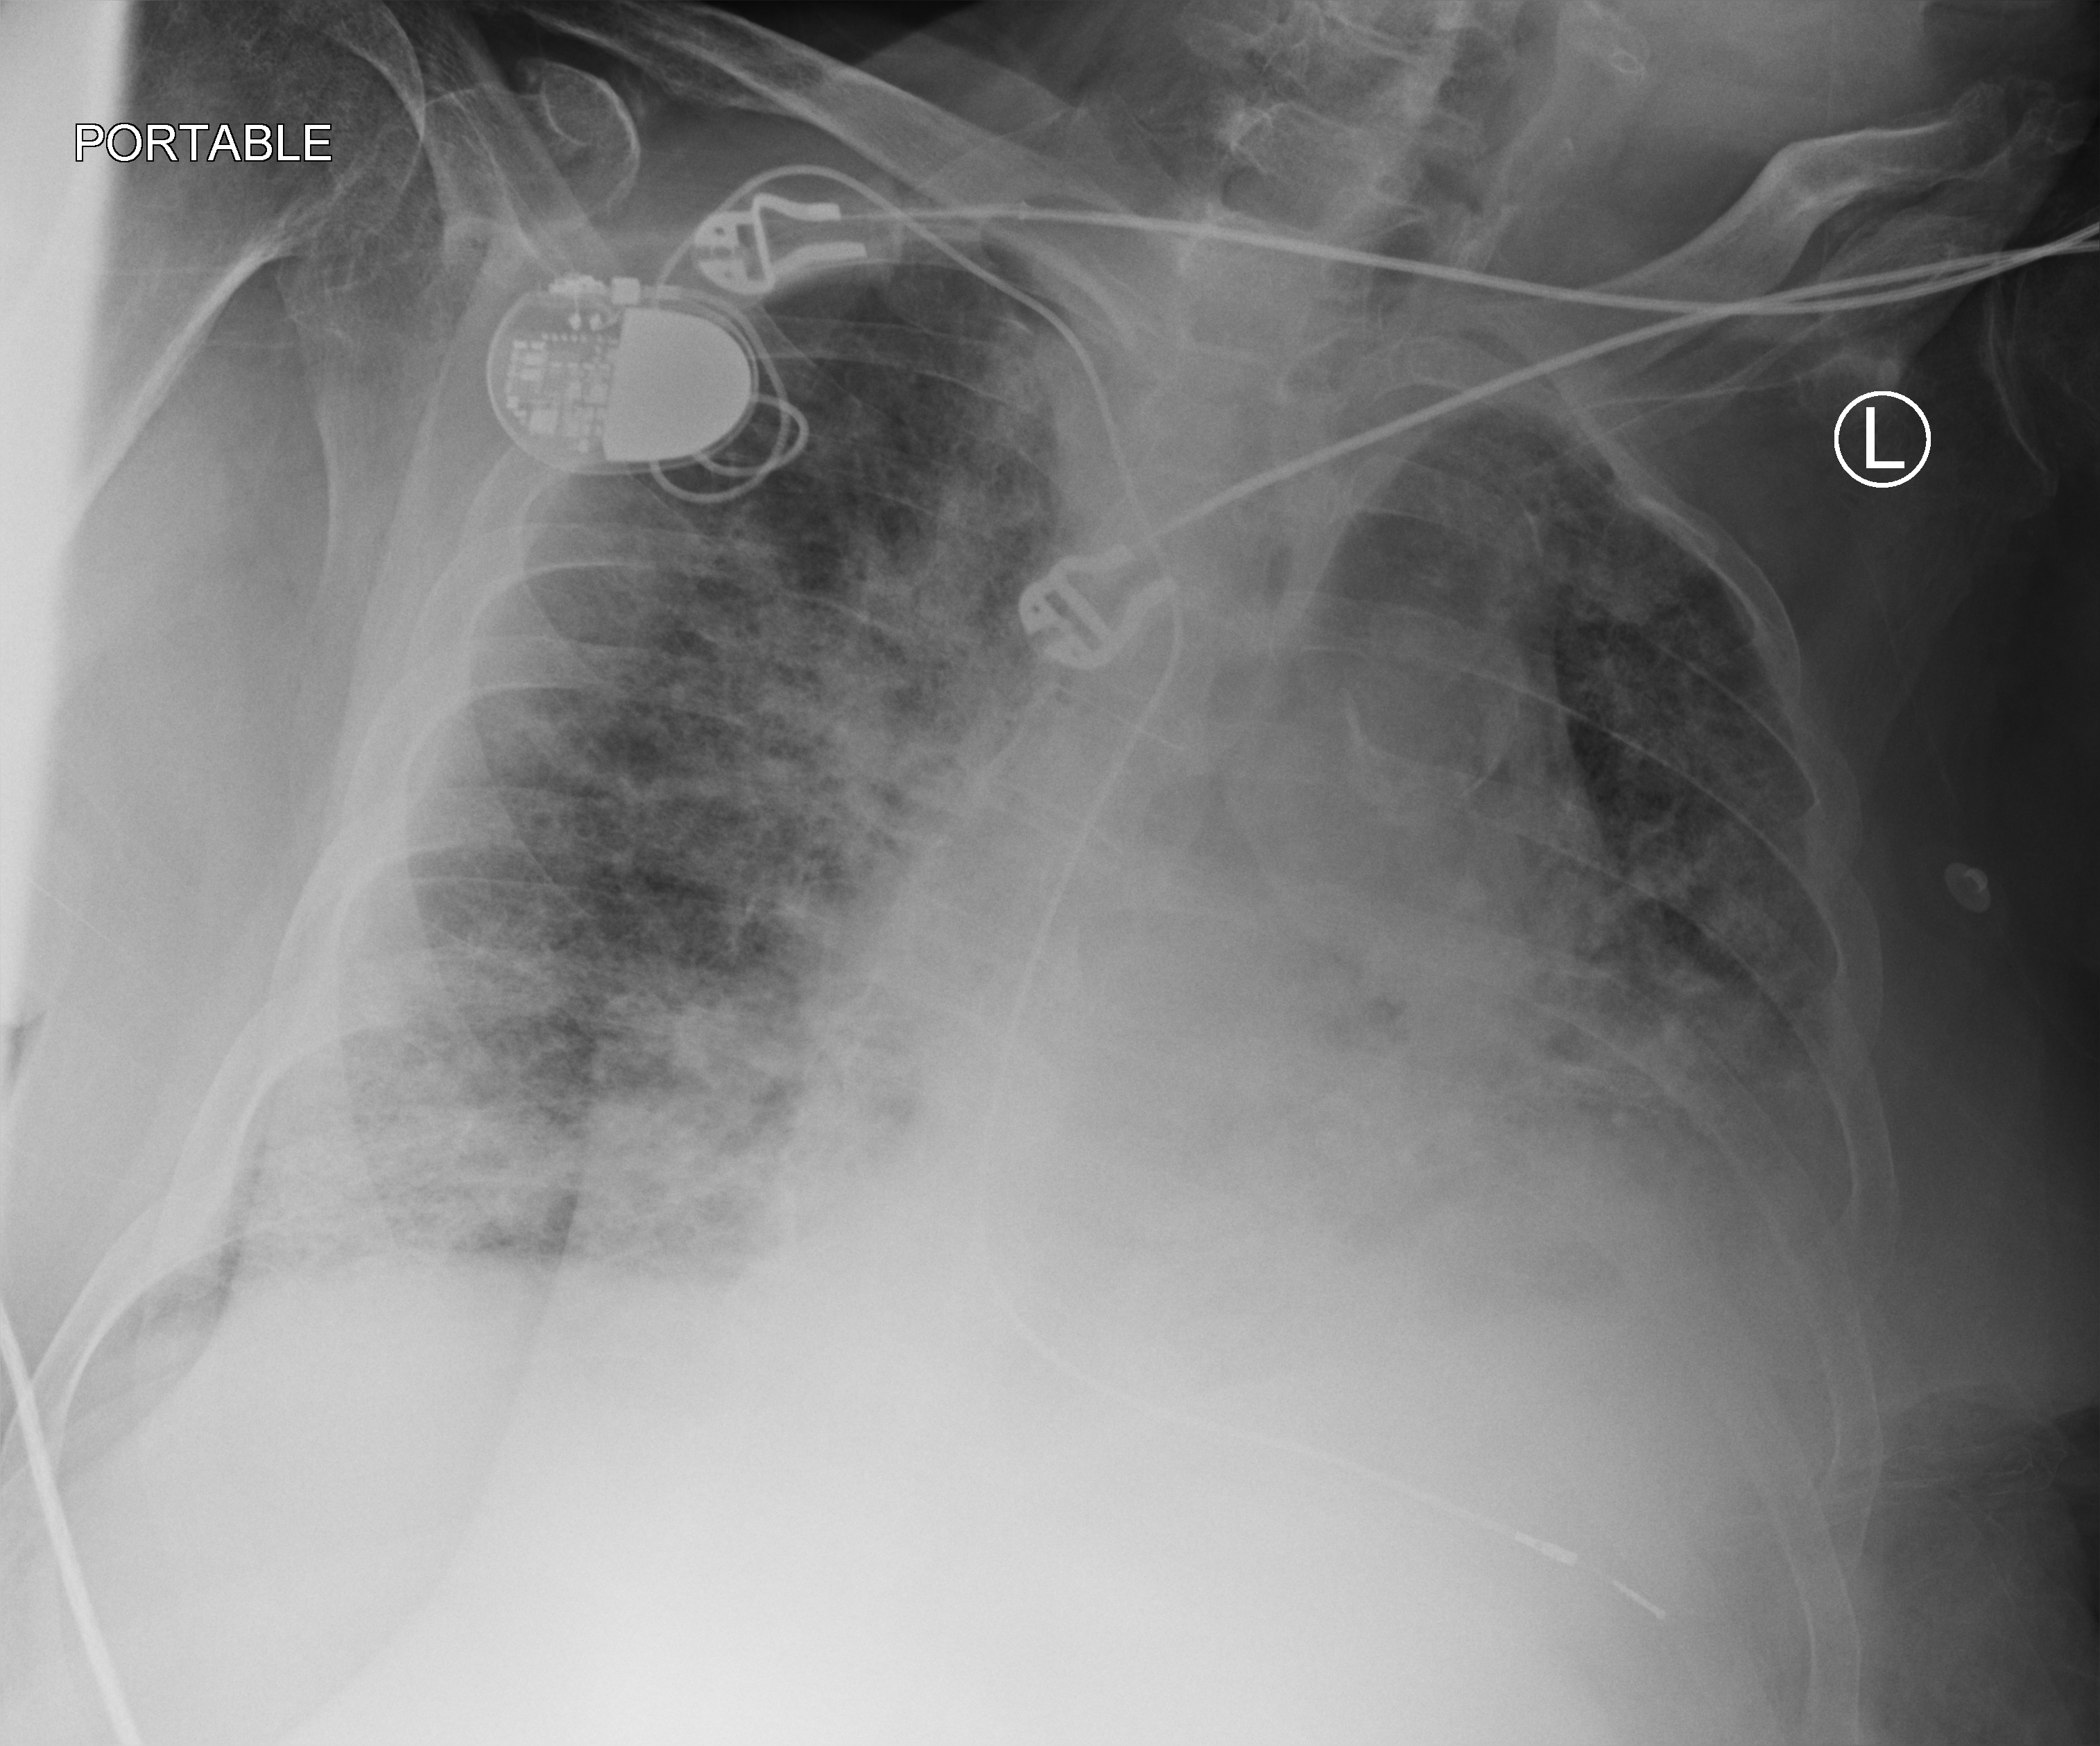
Bedside chest radiograph (computed radiography); anteroposterior (AP) projection. Male patient hospitalised with COVID-19, age 75–90 years.
Hospital-stay facts (about this admission, not read from this image; timing relative to this image not recorded):
- COPD (admission record): no
- admitted to intensive care during this hospital stay: no
- mechanically ventilated during this hospital stay: no